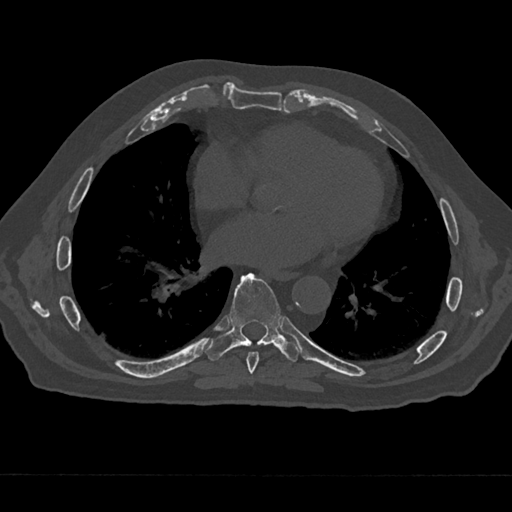
CT including the spine, one axial slice. Slice 335 of 797 in the series (ordered by position). Bone window (W 1800 / L 400 HU). 0.5 mm slice thickness. 512 × 512 image matrix, field of view 377 × 377 mm. Male patient, age 75 years. Case-level facts recorded for this patient, not image findings: primary cancer: renal.
Annotated regions visible in this slice (semi-automatic segmentation, software-assisted and operator-edited):
- T7 vertebra: bounding box [x1, y1, x2, y2] px = [246, 351, 259, 378]
- T8 vertebra: [206, 272, 300, 362]